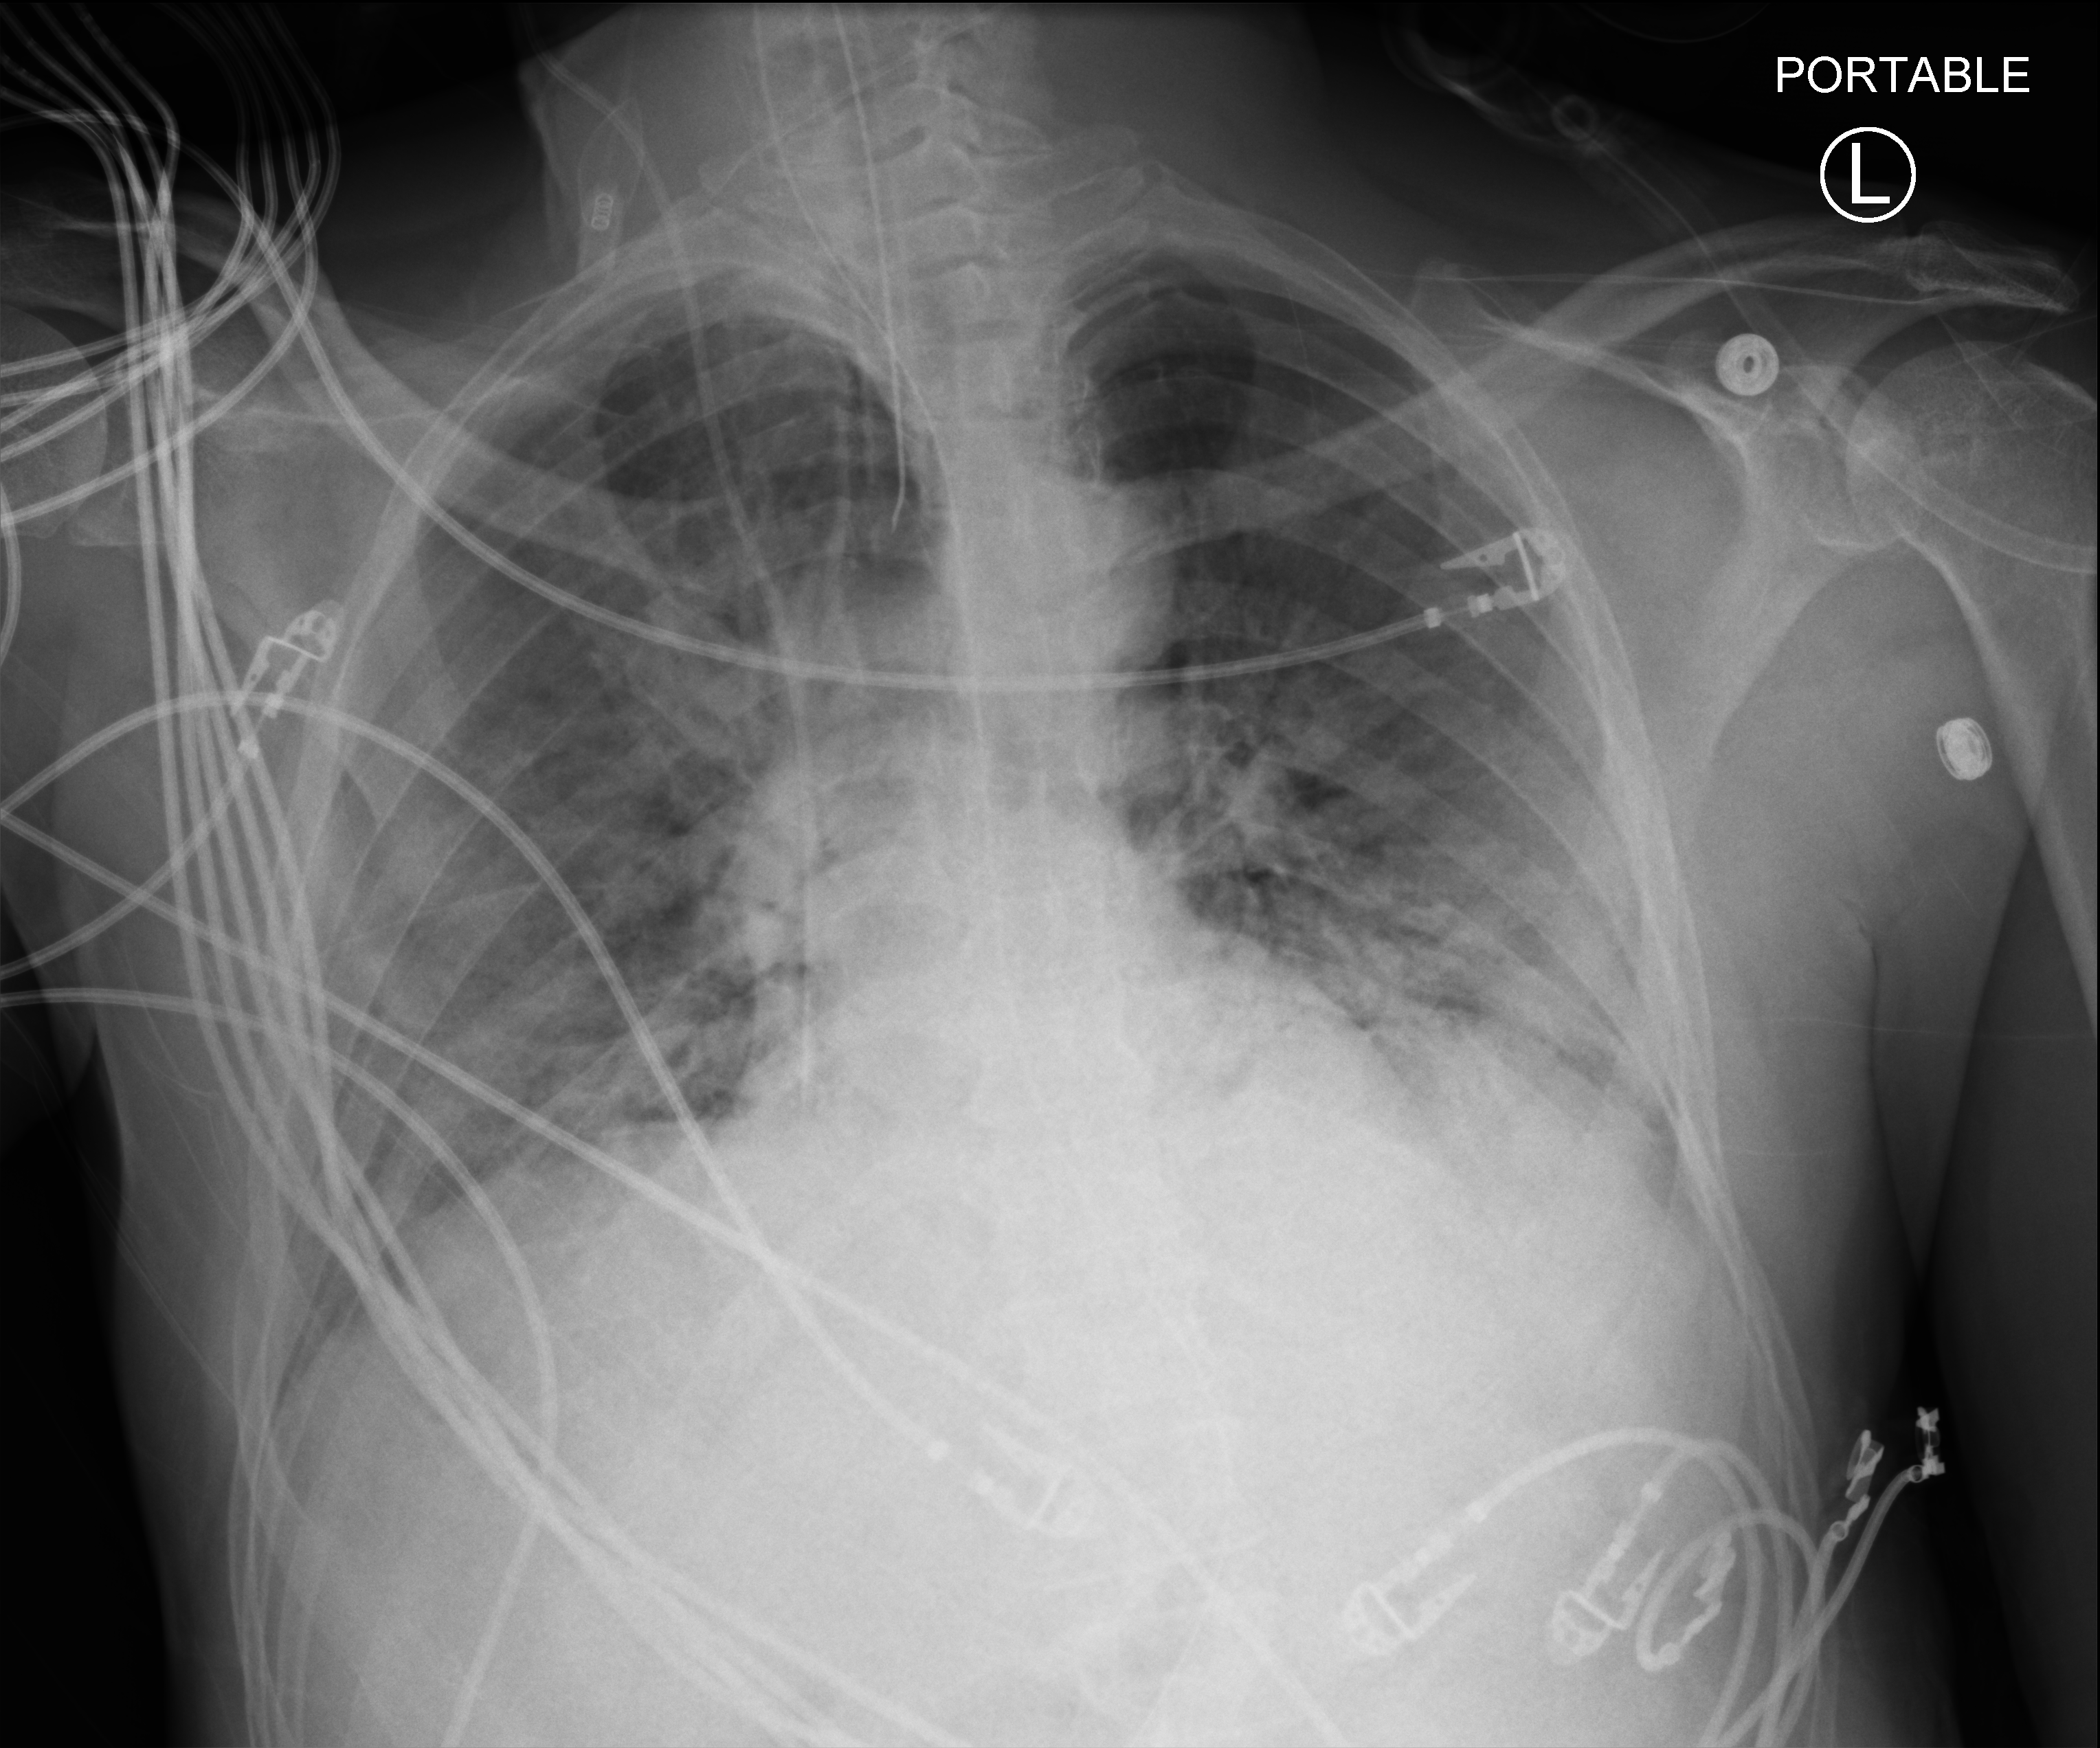
Portable chest radiograph; anteroposterior (AP) projection. Patient hospitalised with COVID-19; male, aged 18–59 years.
From the hospital-stay record, not from the radiograph (when in the stay this image was taken is not recorded): mechanically ventilated during this hospital stay: yes; length of hospital stay: 41 days.